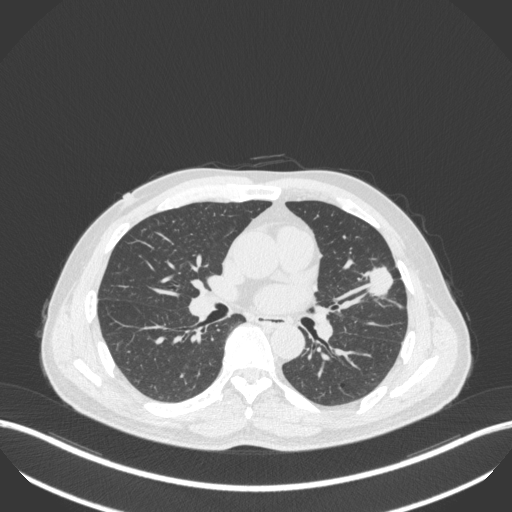
Chest CT, one axial slice. Slice 213 of 418 in the series (ordered by position). Lung window (W 1500 / L -600 HU). 1 mm slice thickness. 512 × 512 image matrix, field of view 400 × 400 mm. Patient: male, 55 years. Case-level facts recorded for this patient, not image findings: clinical TNM (as recorded): T1c N0 M0.
Structures marked on this image (bounding box drawn by a radiologist):
- lung tumour (recorded histology: adenocarcinoma): bounding box [x1, y1, x2, y2] px = [363, 265, 395, 302]